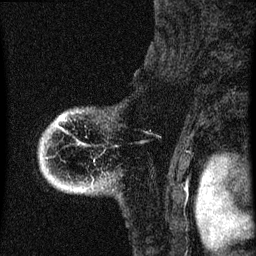
Breast MRI (dynamic contrast-enhanced), one sagittal slice. Slice 56 of 60 in the series (ordered by position). Dynamic contrast-enhanced series, image 2 of 4 at this slice position (ordered by acquisition). 1.5 T. TE 4.2 ms, TR 8 ms. 2 mm slice thickness. 256 × 256 image matrix, field of view 180 × 180 mm. Female patient, age 71 years.
Structures marked on this image (semi-automatic segmentation, software-assisted and operator-edited):
- analysis volume of interest (the breast-tissue region the enhancement analysis was run in; not a lesion): box from (x=38, y=108) to (x=122, y=201) px
- tumour enhancement mask (voxels above the 70 % enhancement threshold inside the analysis volume of interest): (x=59, y=116)–(x=61, y=119)